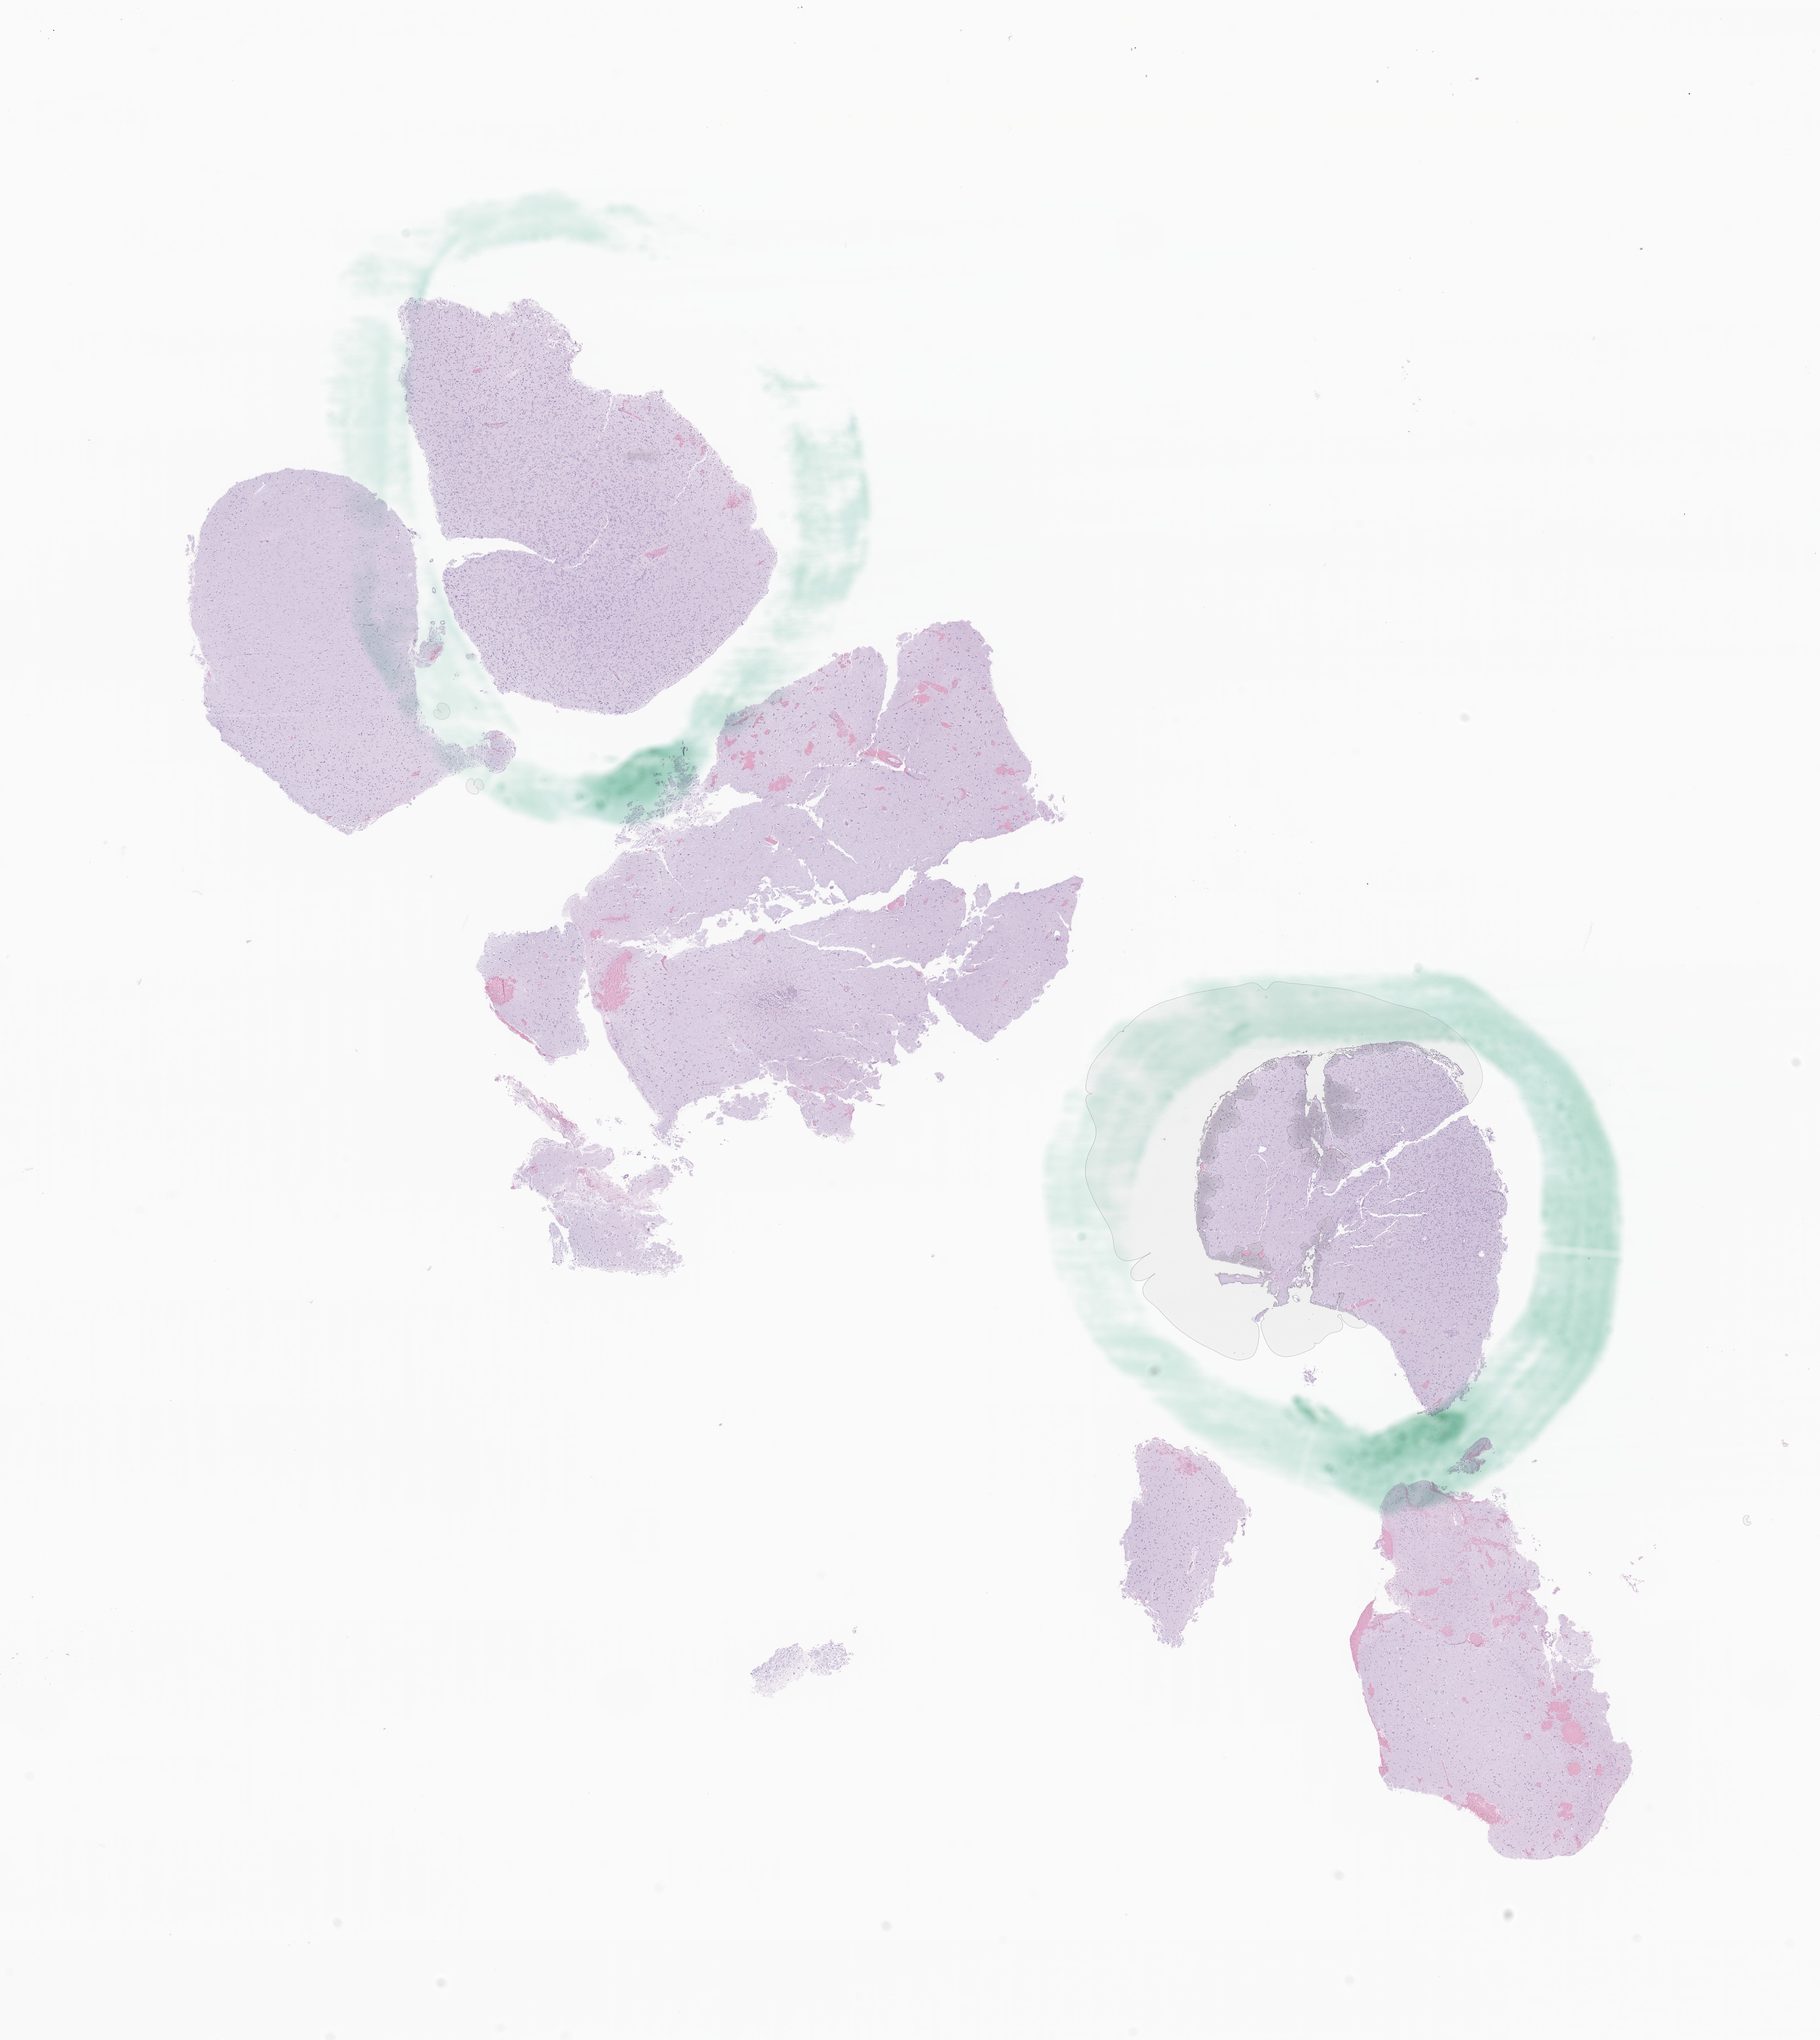
Hematoxylin and eosin (H&E) whole-slide image of tumor tissue from the brain — whole scanned area (about 18.2 x 20.4 mm) shown as a low-resolution overview. Formalin-fixed paraffin-embedded section. Patient: male, age 201 months.
* diagnosis: Neoplasm, uncertain whether benign or malignant